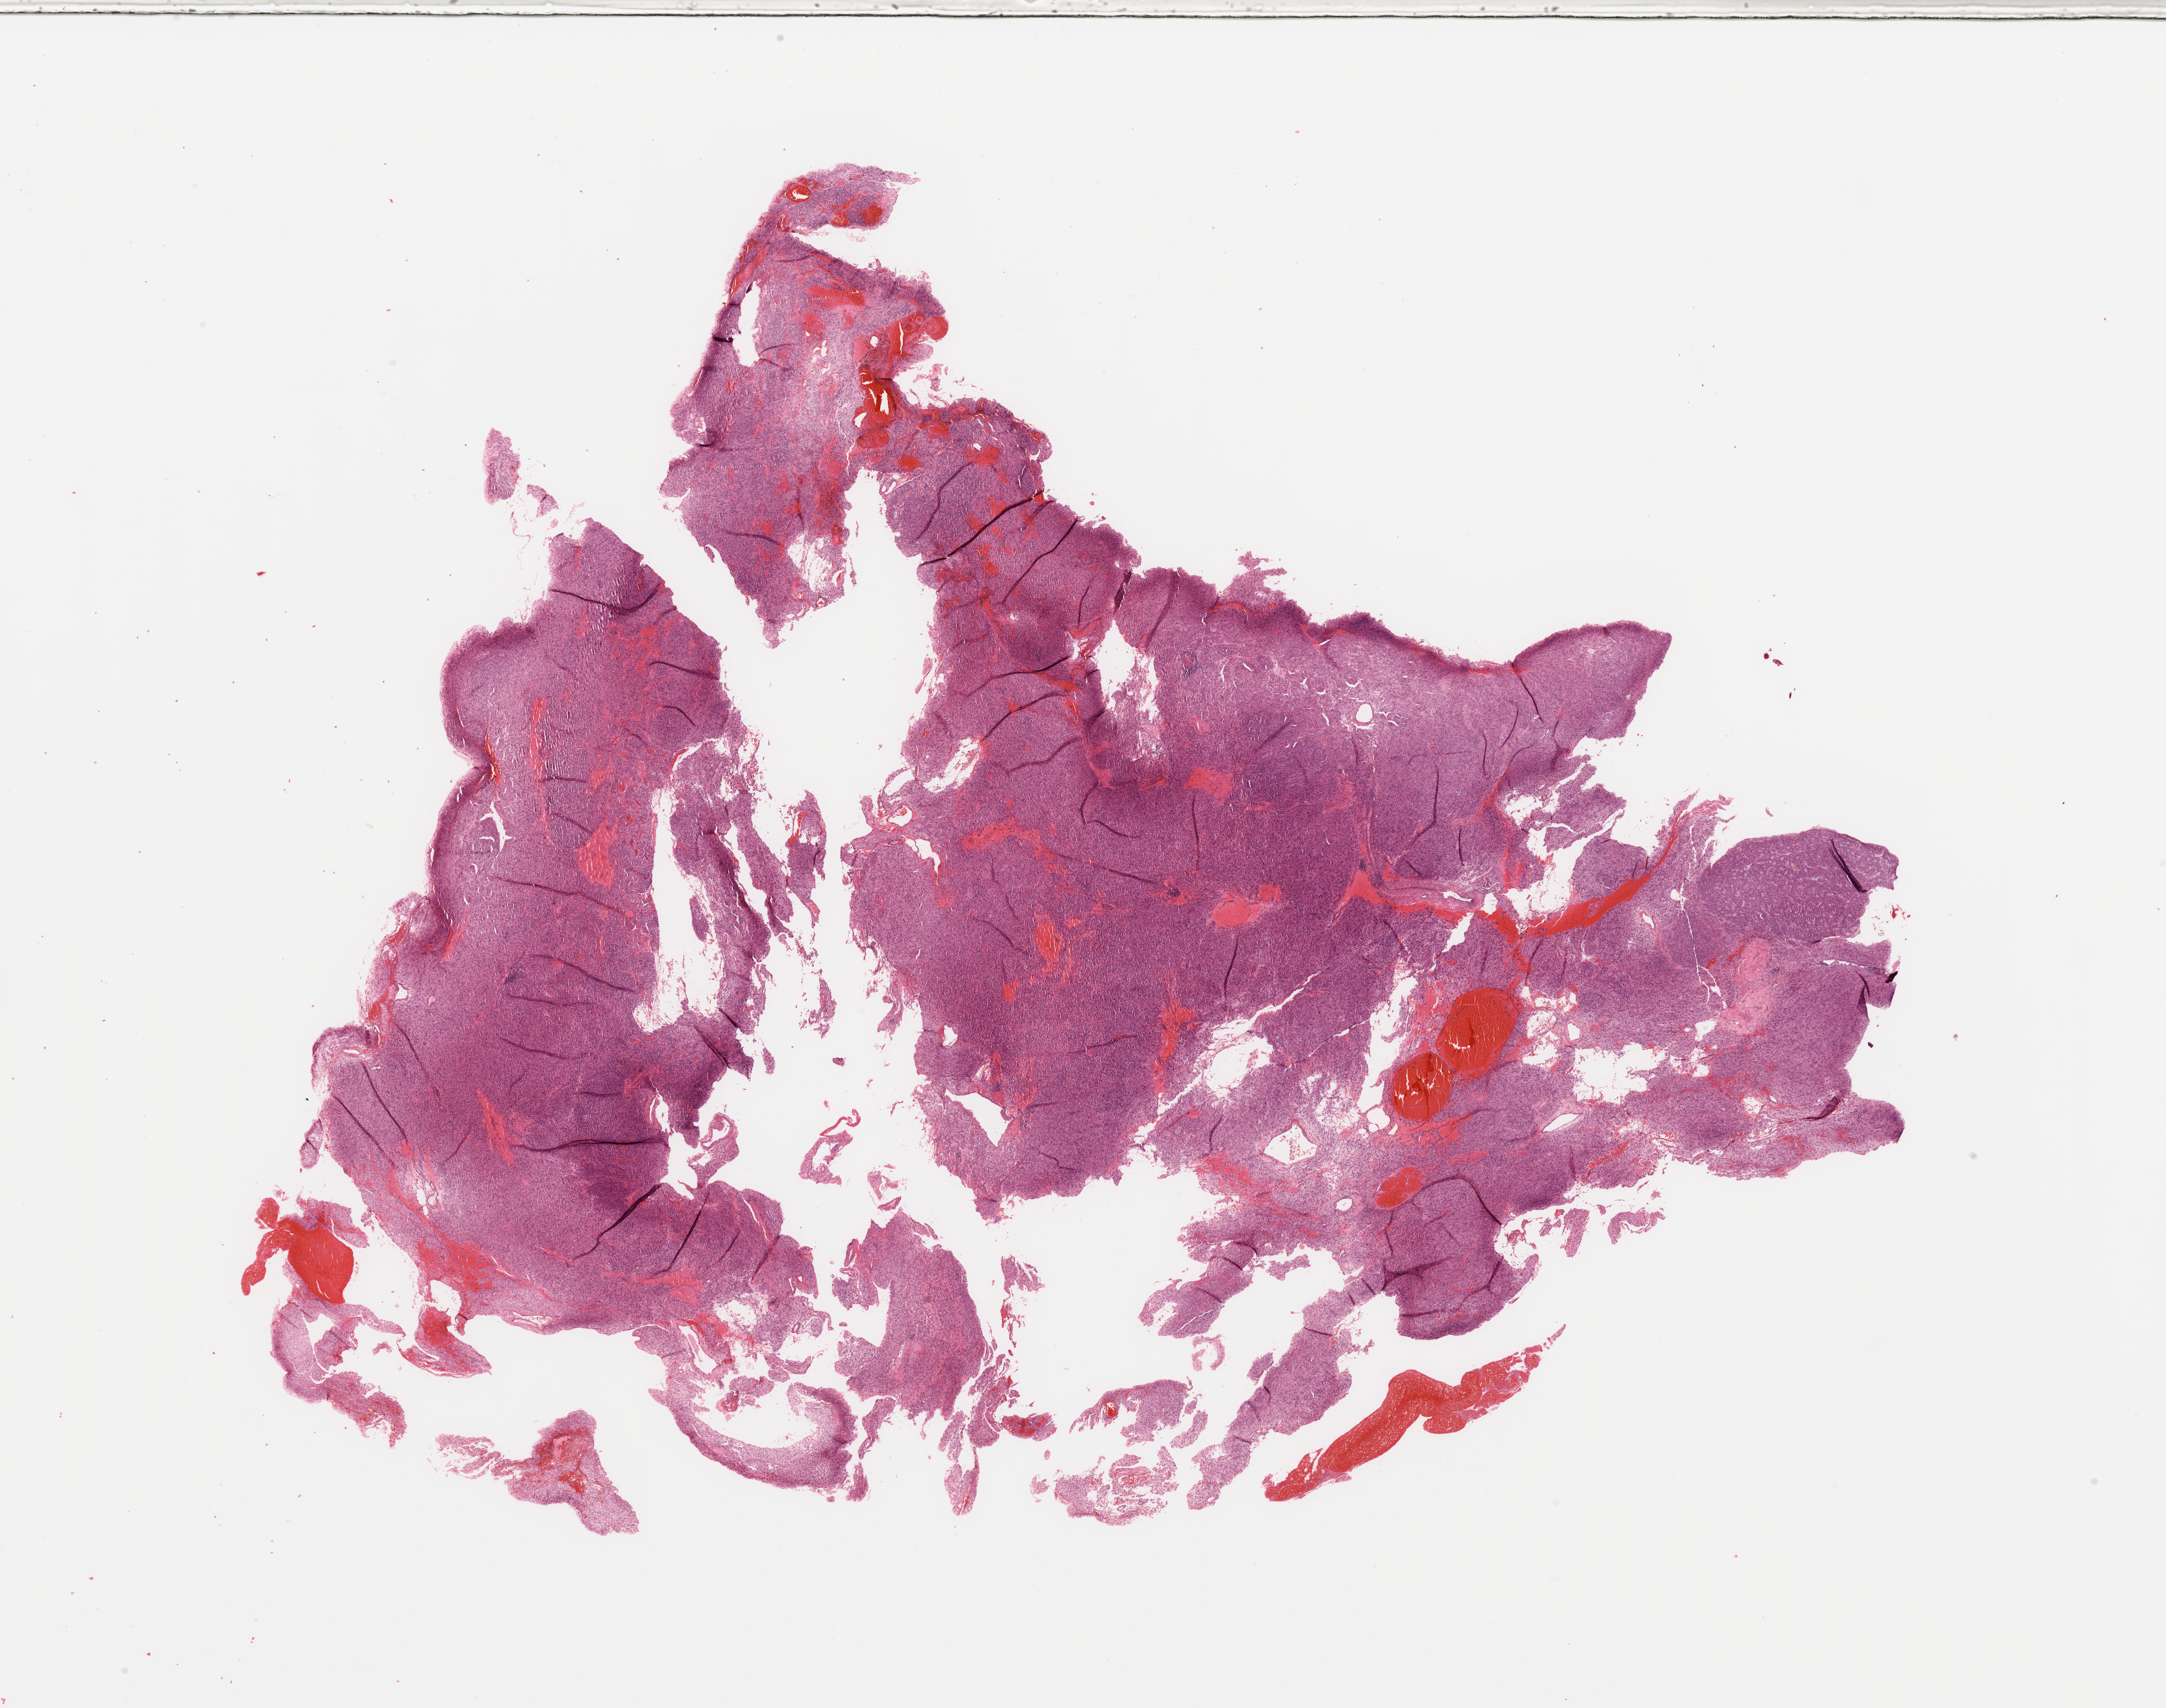
Whole-slide histology image, H&E — whole scanned area (about 26.6 x 21.0 mm) shown as a low-resolution overview. 73-year-old female patient.
- patient diagnosis (cohort enrolment): sarcoma (site not recorded at cohort level)